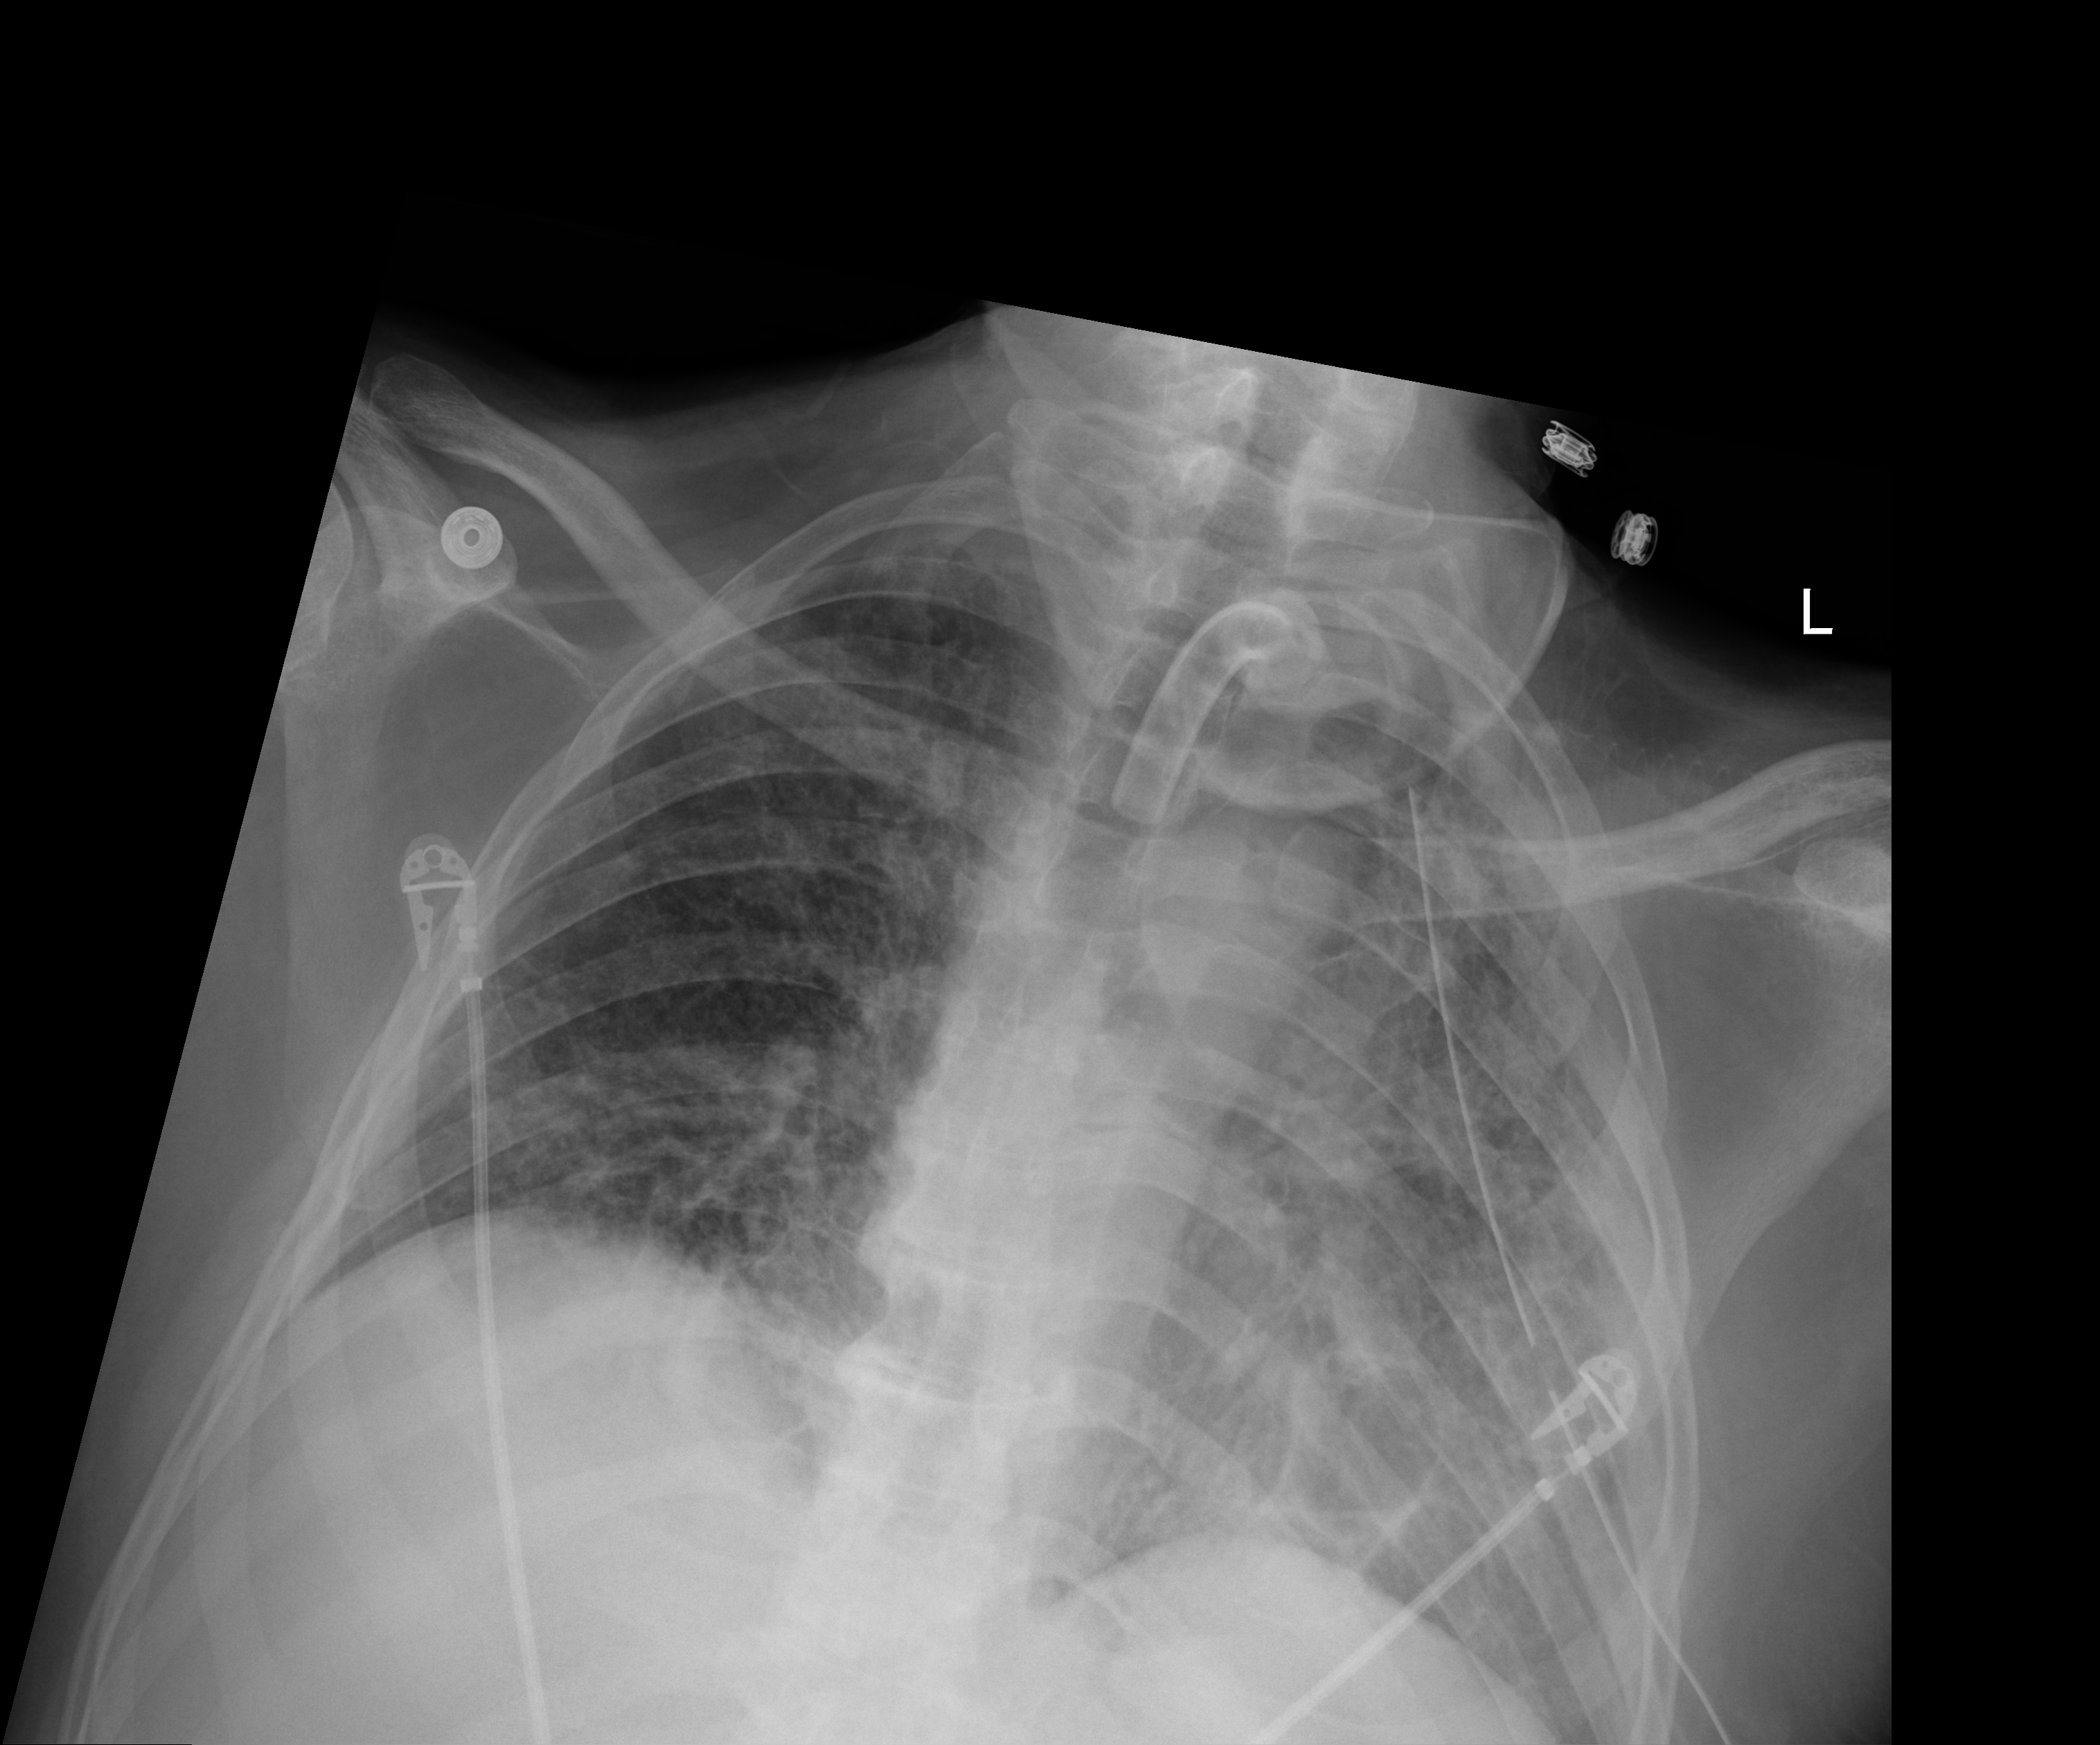
Bedside chest radiograph (digital radiography). Patient hospitalised with COVID-19; male, aged 18–59 years.
From the hospital-stay record, not from the radiograph (when in the stay this image was taken is not recorded): mechanically ventilated during this hospital stay: yes; other chronic lung disease (admission record): no; smoking status (admission record): never.